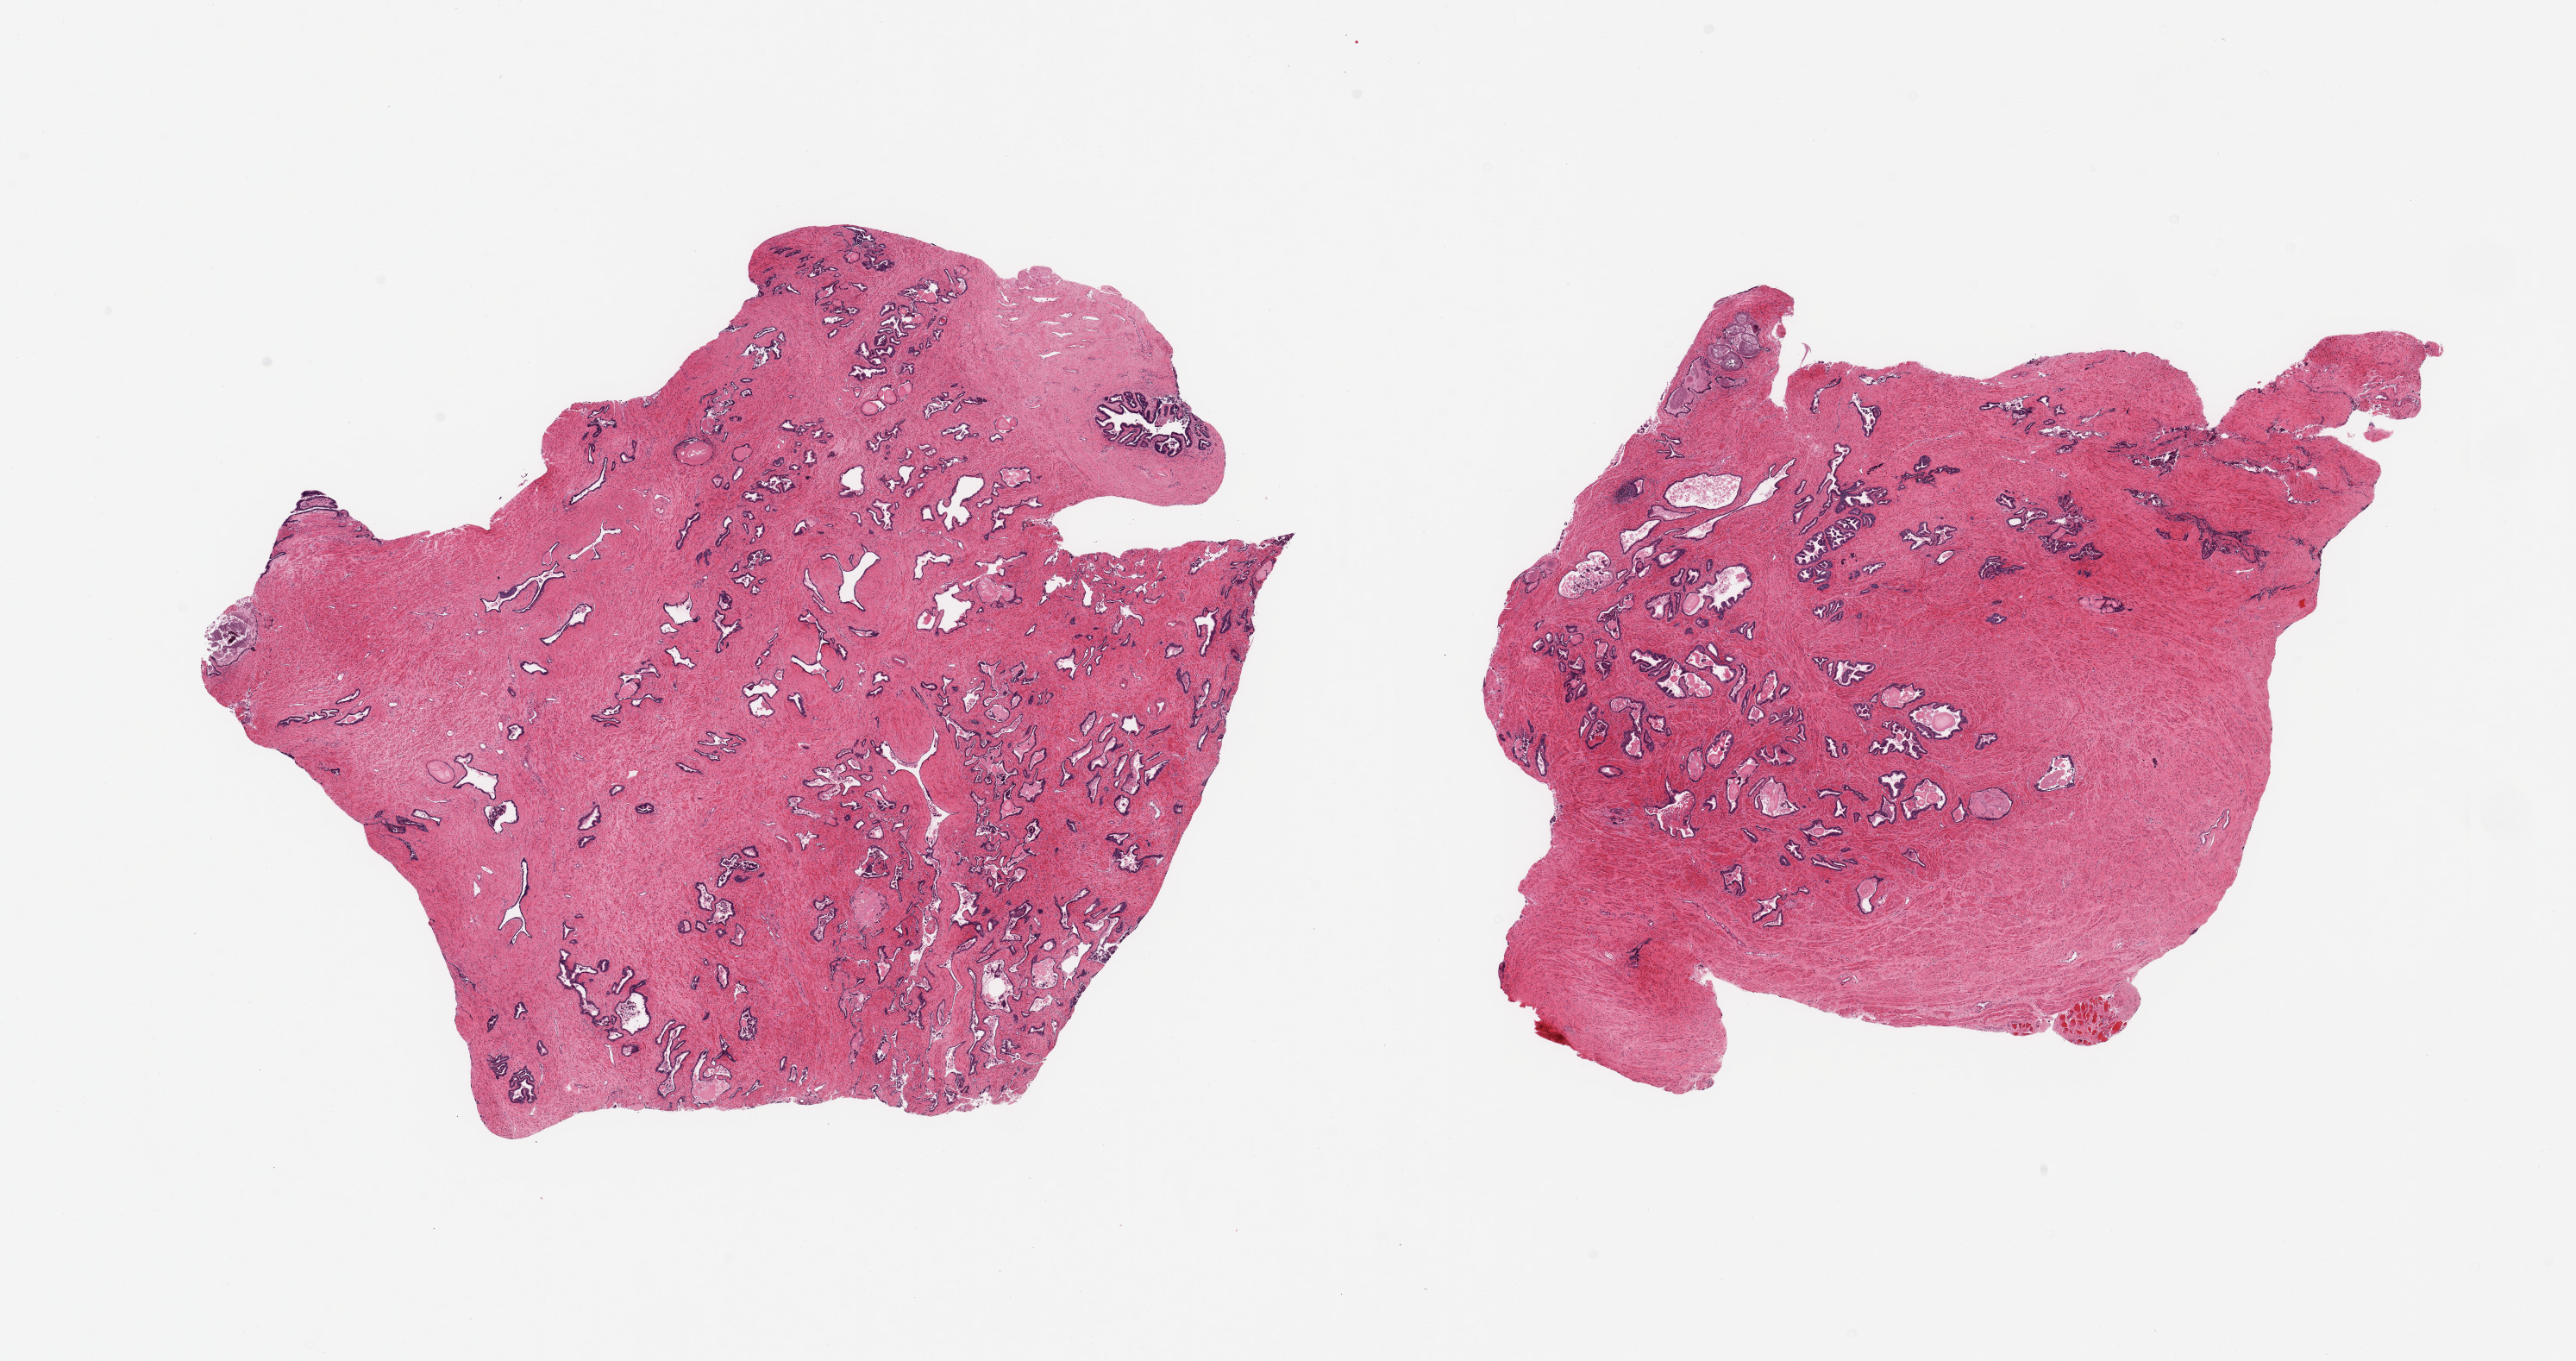
Whole-slide image, hematoxylin and eosin (H&E) stain — a low-resolution overview of the entire scanned area, about 23.6 x 12.5 mm (acquisition: 20x scan); PAXgene-fixed, paraffin-embedded tissue; target tissue: prostate; donor tissue sample. Male donor.
Reviewer comment on this tissue sample: 2 pieces; more stroma than glands: 70:30.